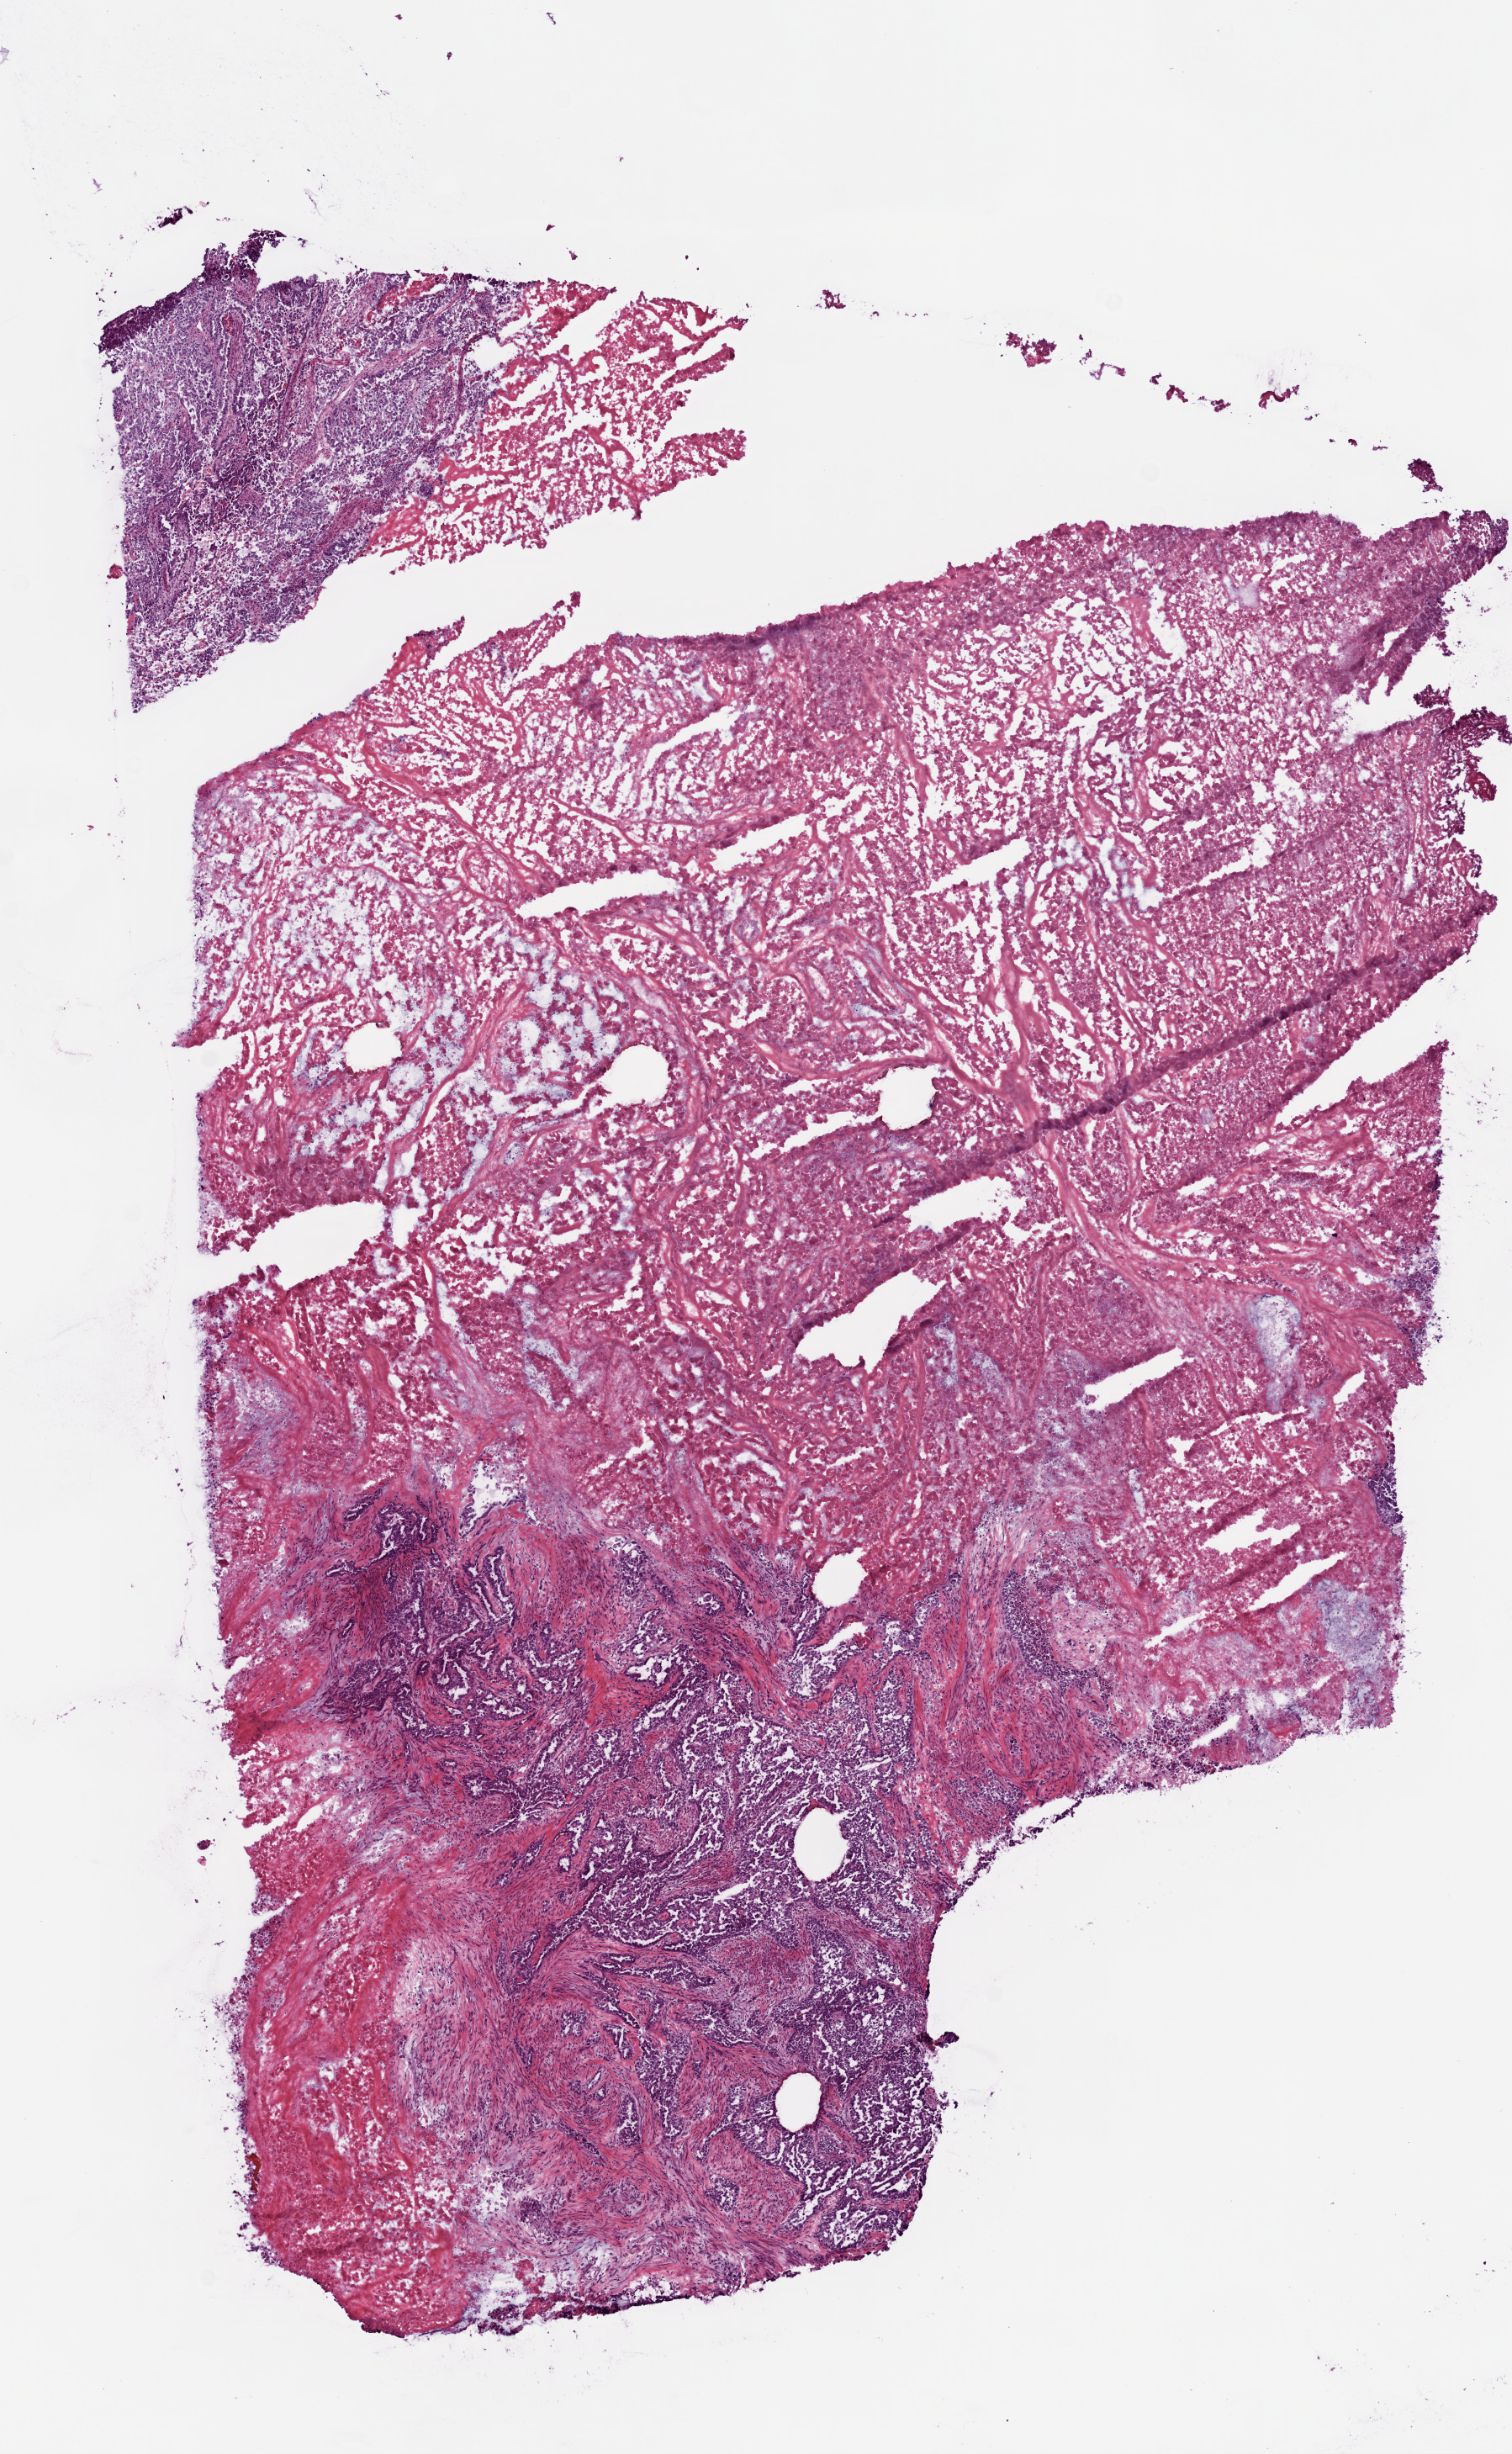
Whole-slide histology image, H&E-stained, shown as a low-resolution overview of the whole scanned area (about 7.3 x 11.8 mm, from a 20x scan); frozen section from the top of the tissue portion; primary tumour sample from the uterus. Female patient; age at initial diagnosis 74 years. Pathologist review of this section (percent, as recorded): tumour cells 75%, tumour nuclei 70%.
Diagnosis: Serous cystadenocarcinoma, NOS.